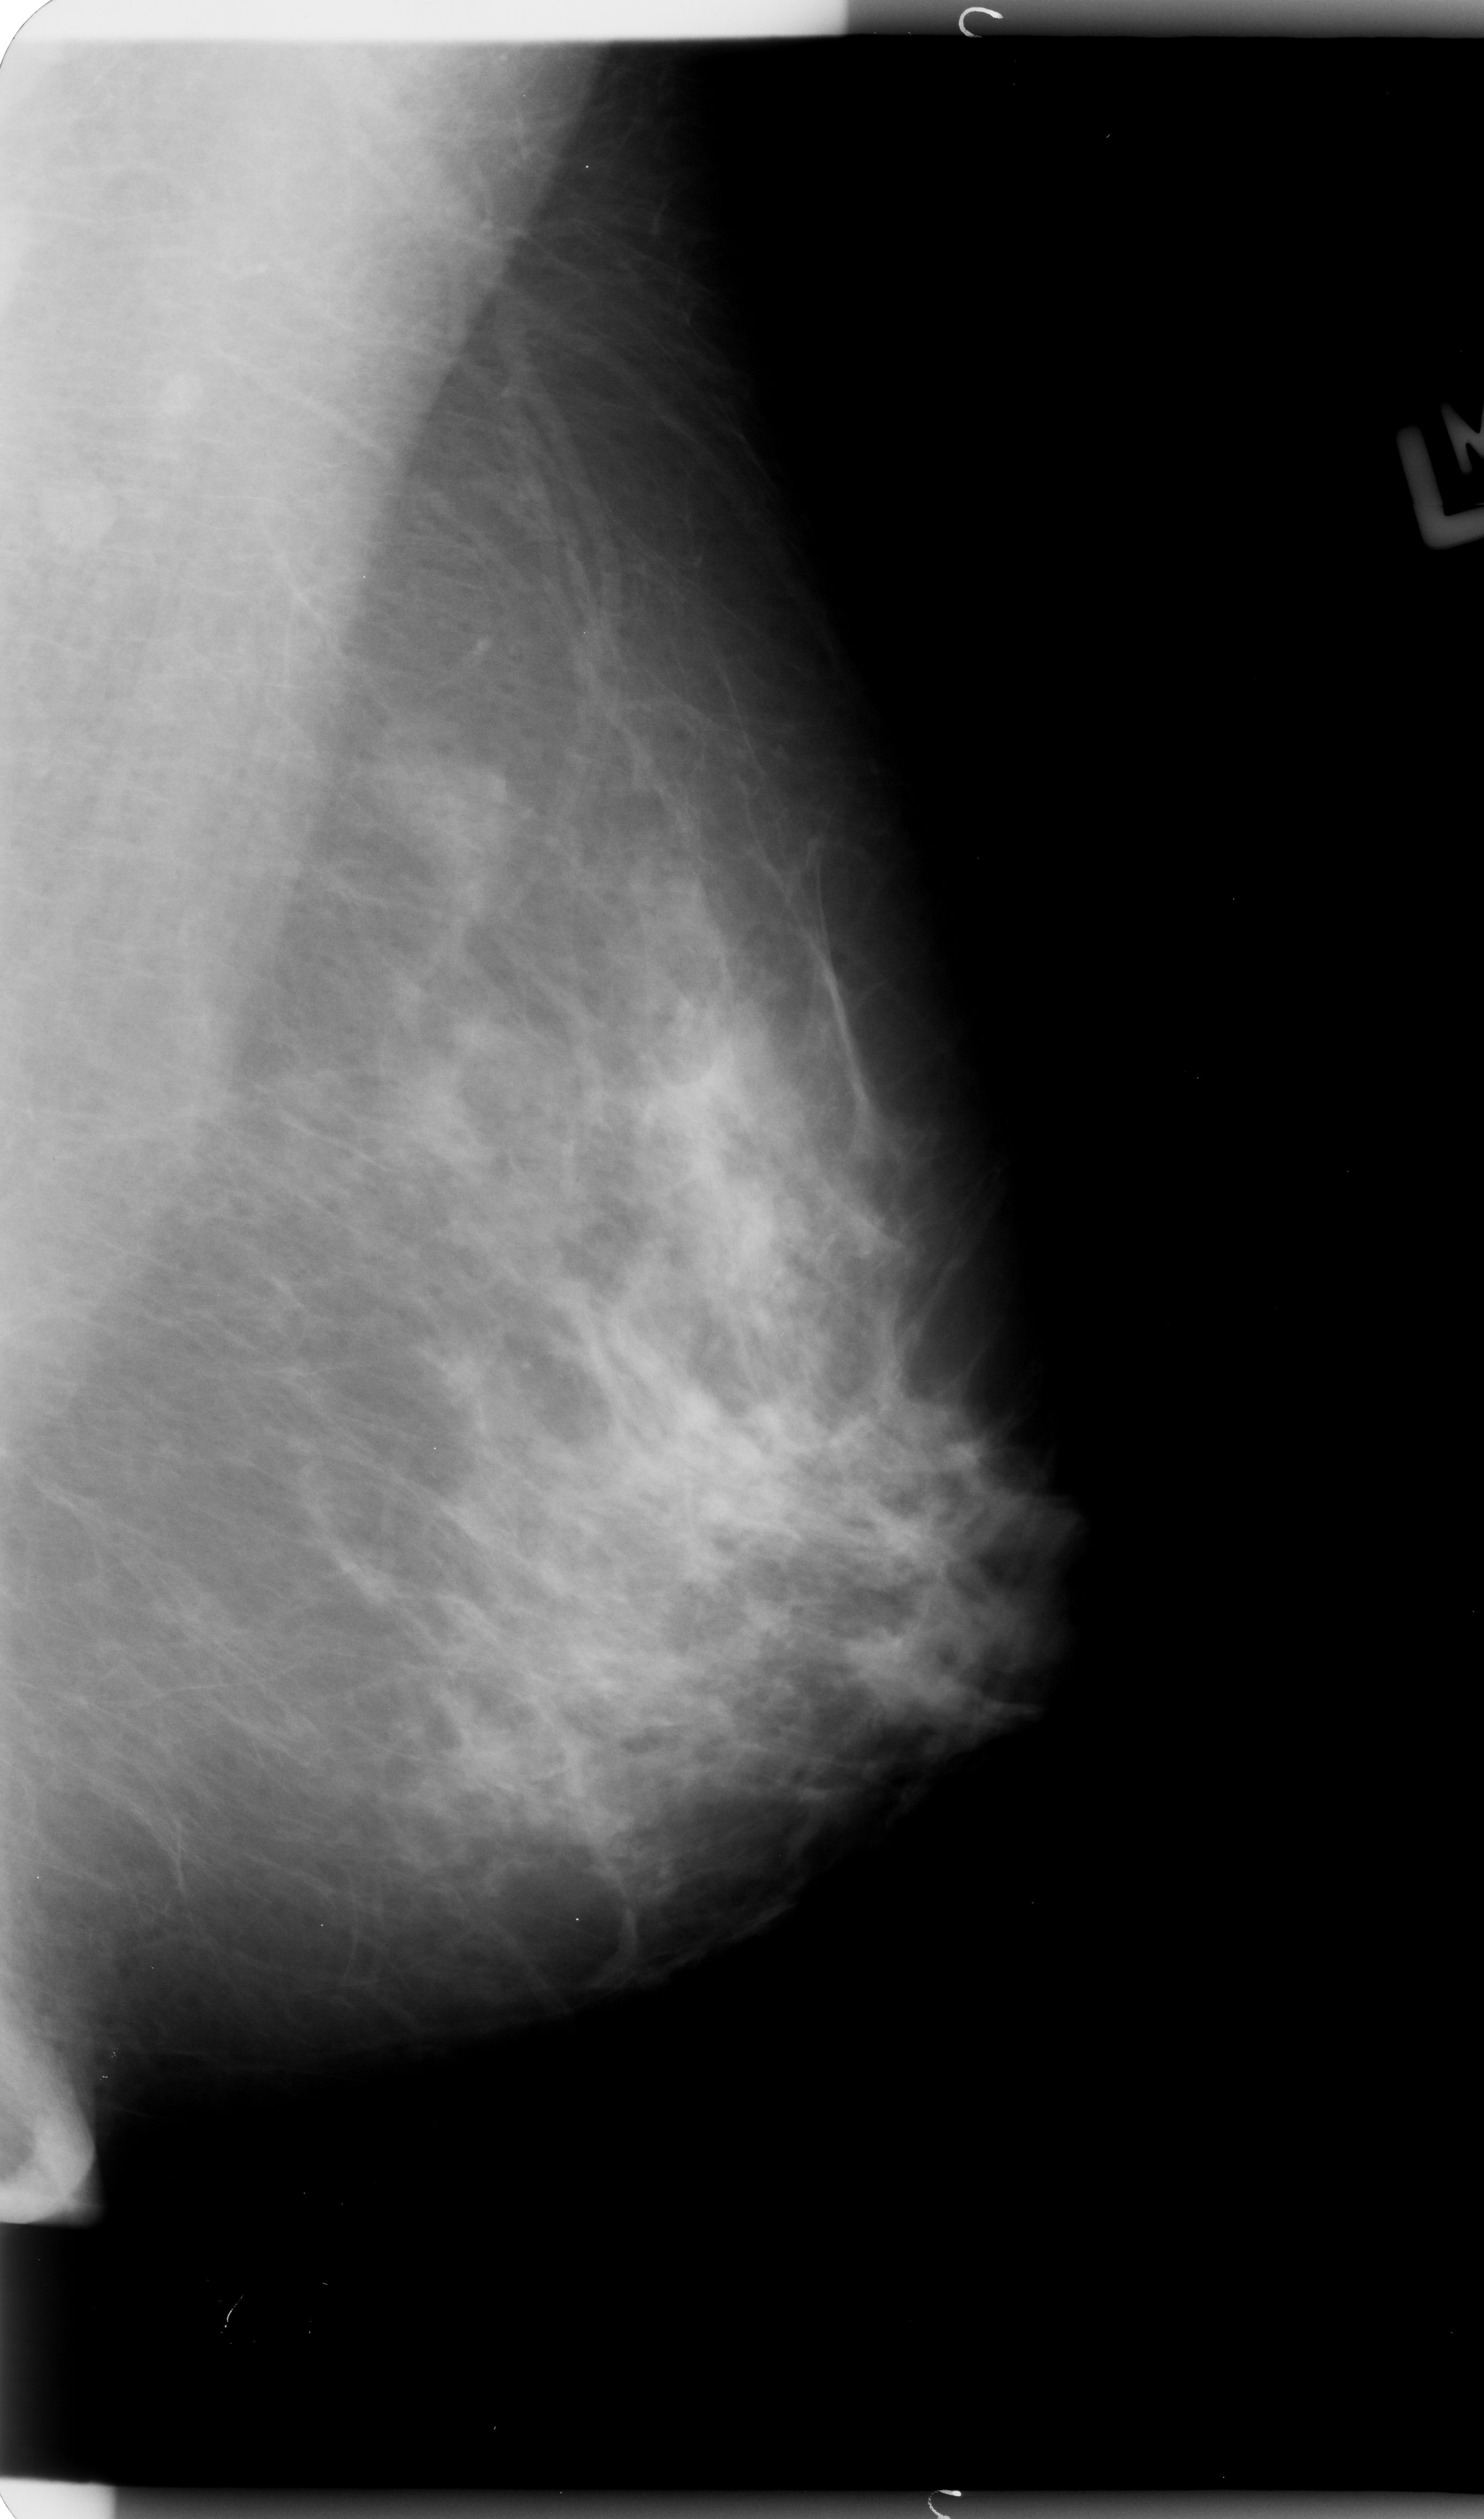
Digitized screen-film mammogram. Left breast. MLO view. Breast composition: heterogeneously dense (BI-RADS density category 3 of 4). 1484 × 2519 image matrix.
Expert-marked regions of interest on this image (one box per marked abnormality):
- mass, shape irregular, margins ill defined; BI-RADS assessment category 3; pathology result (as recorded, not read from the image): benign: box from (x=359, y=732) to (x=491, y=857) px